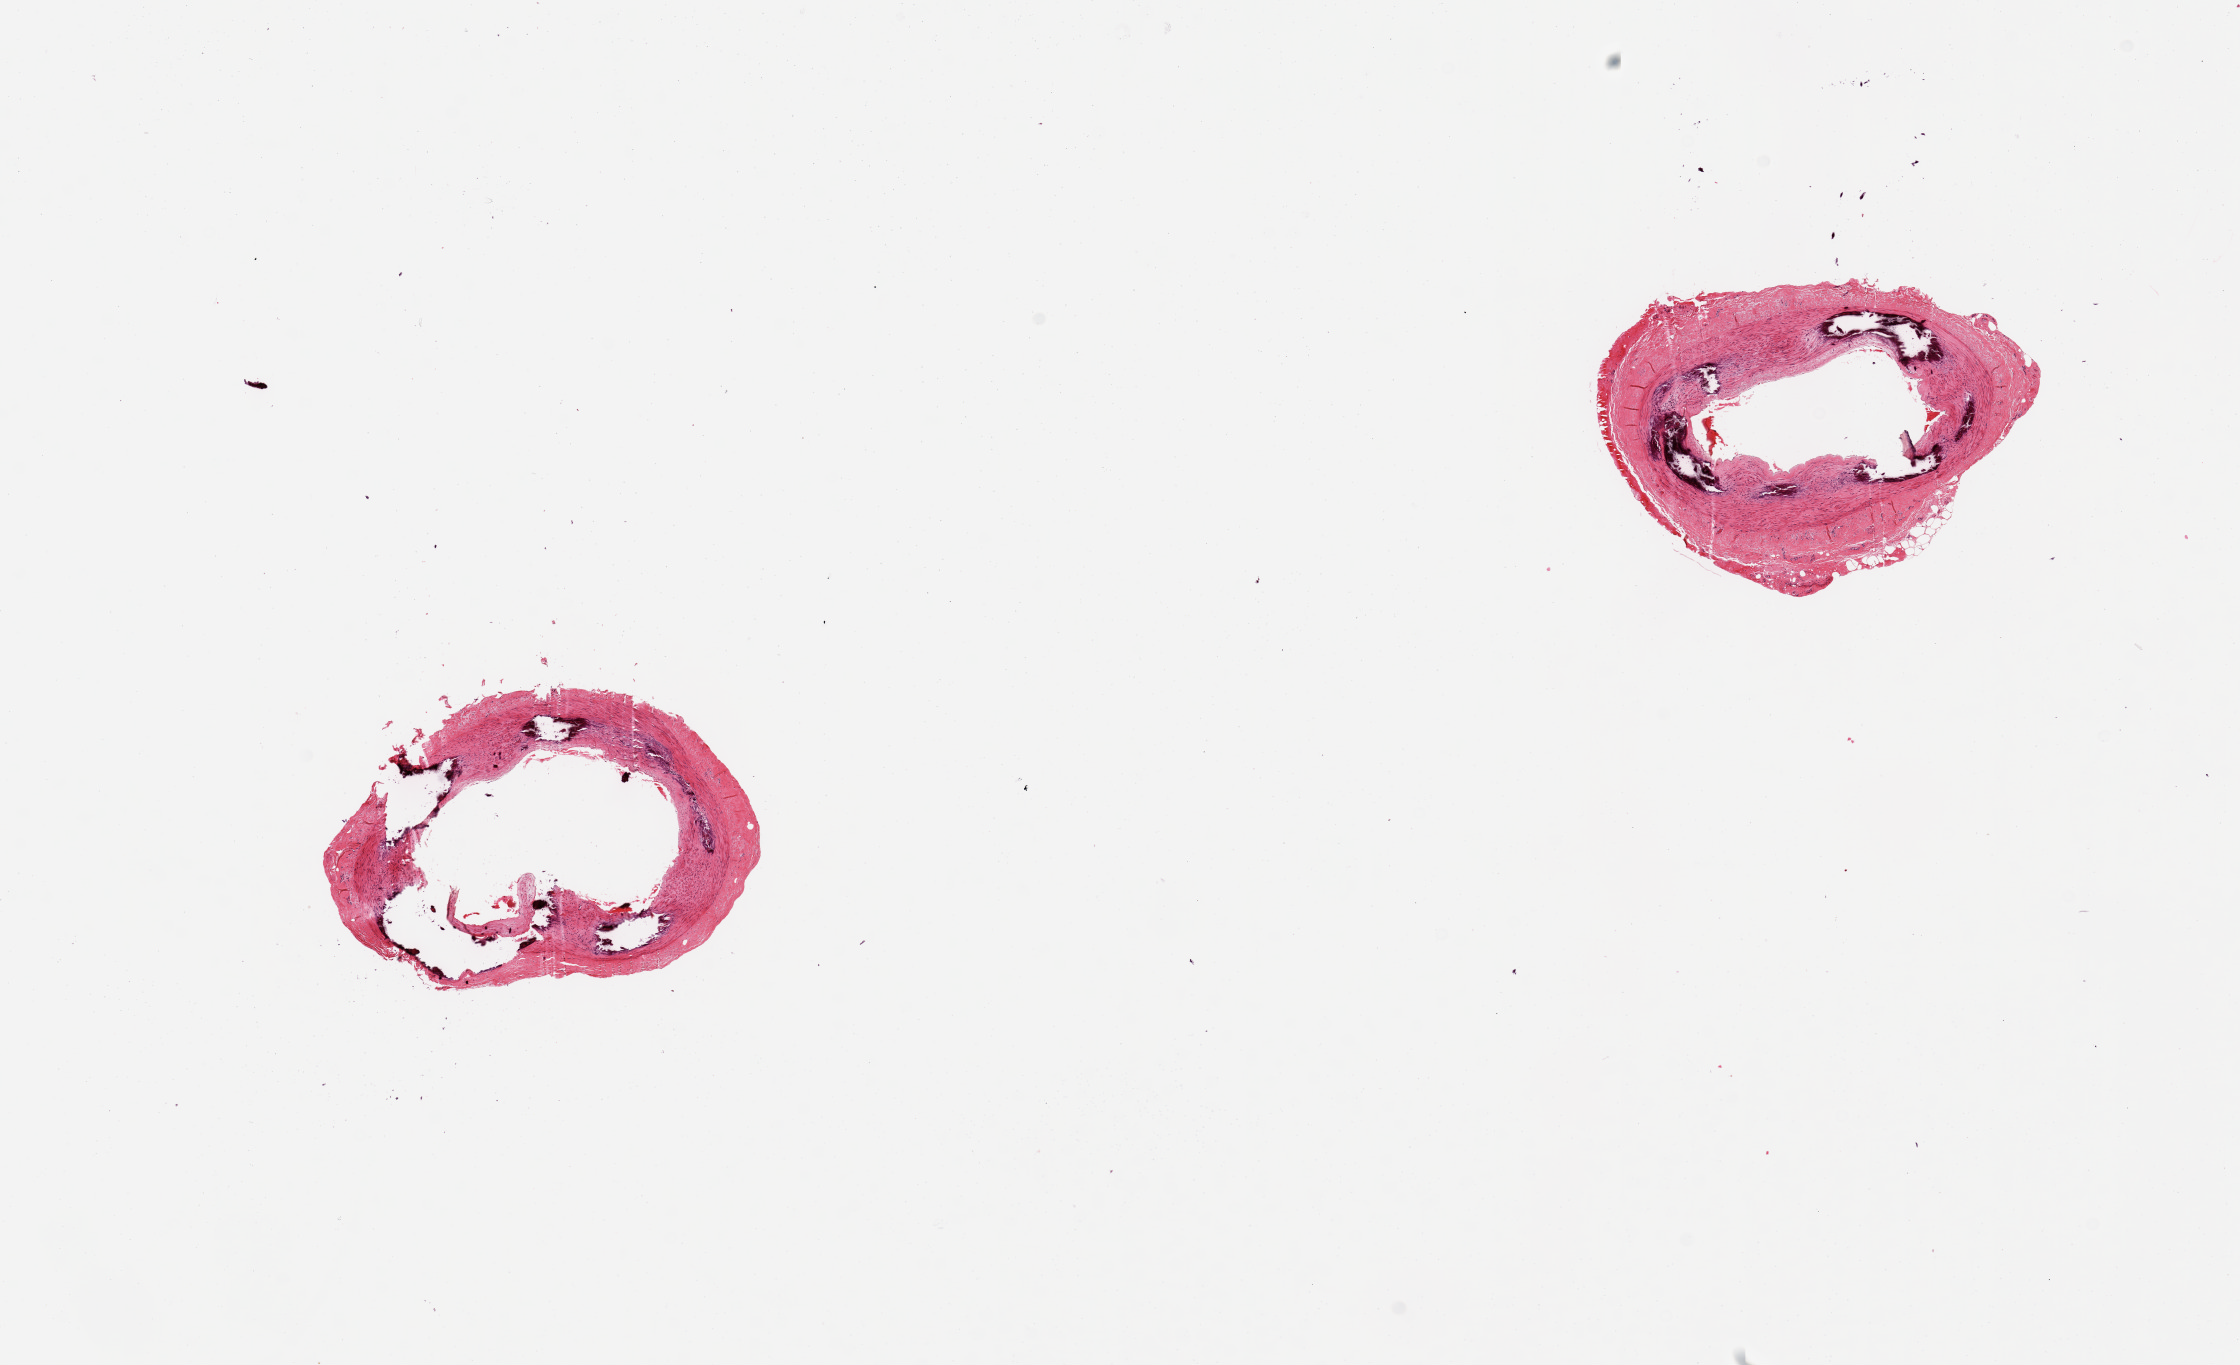
Whole-slide image, H&E stain, low-resolution overview of the scanned area, about 17.7 x 10.8 mm. PAXgene-fixed paraffin-embedded (PFPE) section. Section of tibial artery (target tissue). Donor tissue sample. Male donor.
Review note (as recorded): 2 pieces of Monckeberg's medial sclerosis; minimal atherosis.